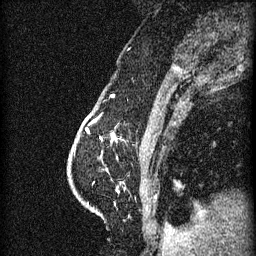
Breast MRI (dynamic contrast-enhanced), one sagittal slice; slice 17 of 60 in the series (ordered by position); 3 images stored at this slice position (order not interpretable as contrast timing); 1.5 T; TE 4.2 ms, TR 11 ms; 256 × 256 image matrix. Patient: female, 63 years.
Annotated regions visible in this slice (semi-automatic segmentation, software-assisted and operator-edited):
- analysis volume of interest (the breast-tissue region the enhancement analysis was run in; not a lesion): box from (x=86, y=118) to (x=125, y=141) px
- tumour enhancement mask (voxels above the 70 % enhancement threshold inside the analysis volume of interest): (x=86, y=128)–(x=115, y=139)